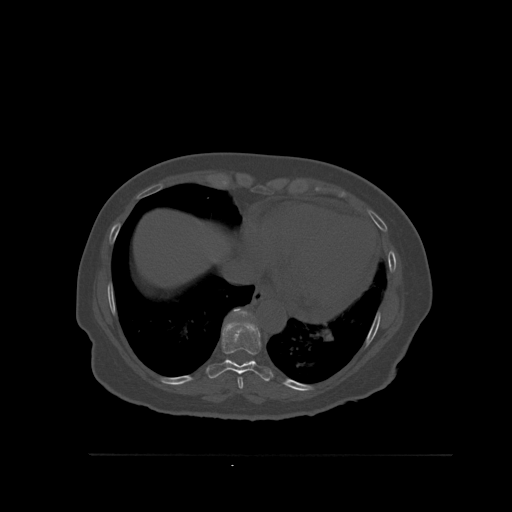
CT including the spine, one axial slice. Position 335 of 527 along the scan axis. Bone window (W 1800 / L 400 HU). 1.5 mm slice thickness. 512 × 512 image matrix, field of view 470 × 470 mm. Patient: female, 73 years. Case-level facts recorded for this patient, not image findings: primary cancer: breast.
Annotated regions visible in this slice (semi-automatically segmented with operator editing):
- T10 vertebra: box from (x=230, y=311) to (x=255, y=318) px
- T8 vertebra: (x=237, y=377)–(x=243, y=389)
- T9 vertebra: (x=206, y=321)–(x=273, y=382)